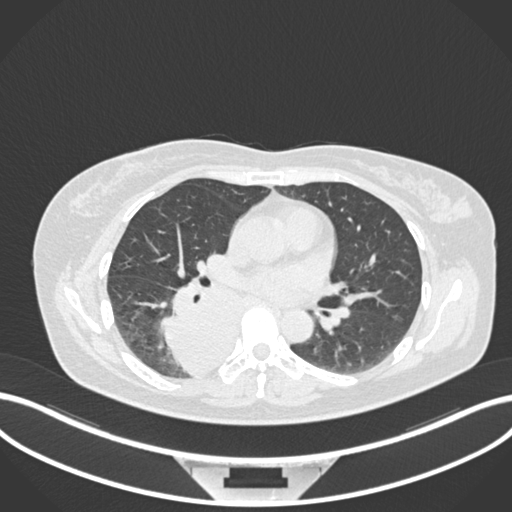
Chest CT, one axial slice; slice 590 of 677 in the series (ordered by position); lung window (W 1500 / L -600 HU); 1 mm slice thickness; 512 × 512 image matrix, field of view 400 × 400 mm. Female patient, age 54 years. From the clinical record (not read from this slice): clinical TNM (as recorded): T4 N0 M0.
Structures marked on this image (bounding box drawn by a radiologist):
- lung tumour (recorded histology: adenocarcinoma): box from (x=158, y=272) to (x=247, y=379) px